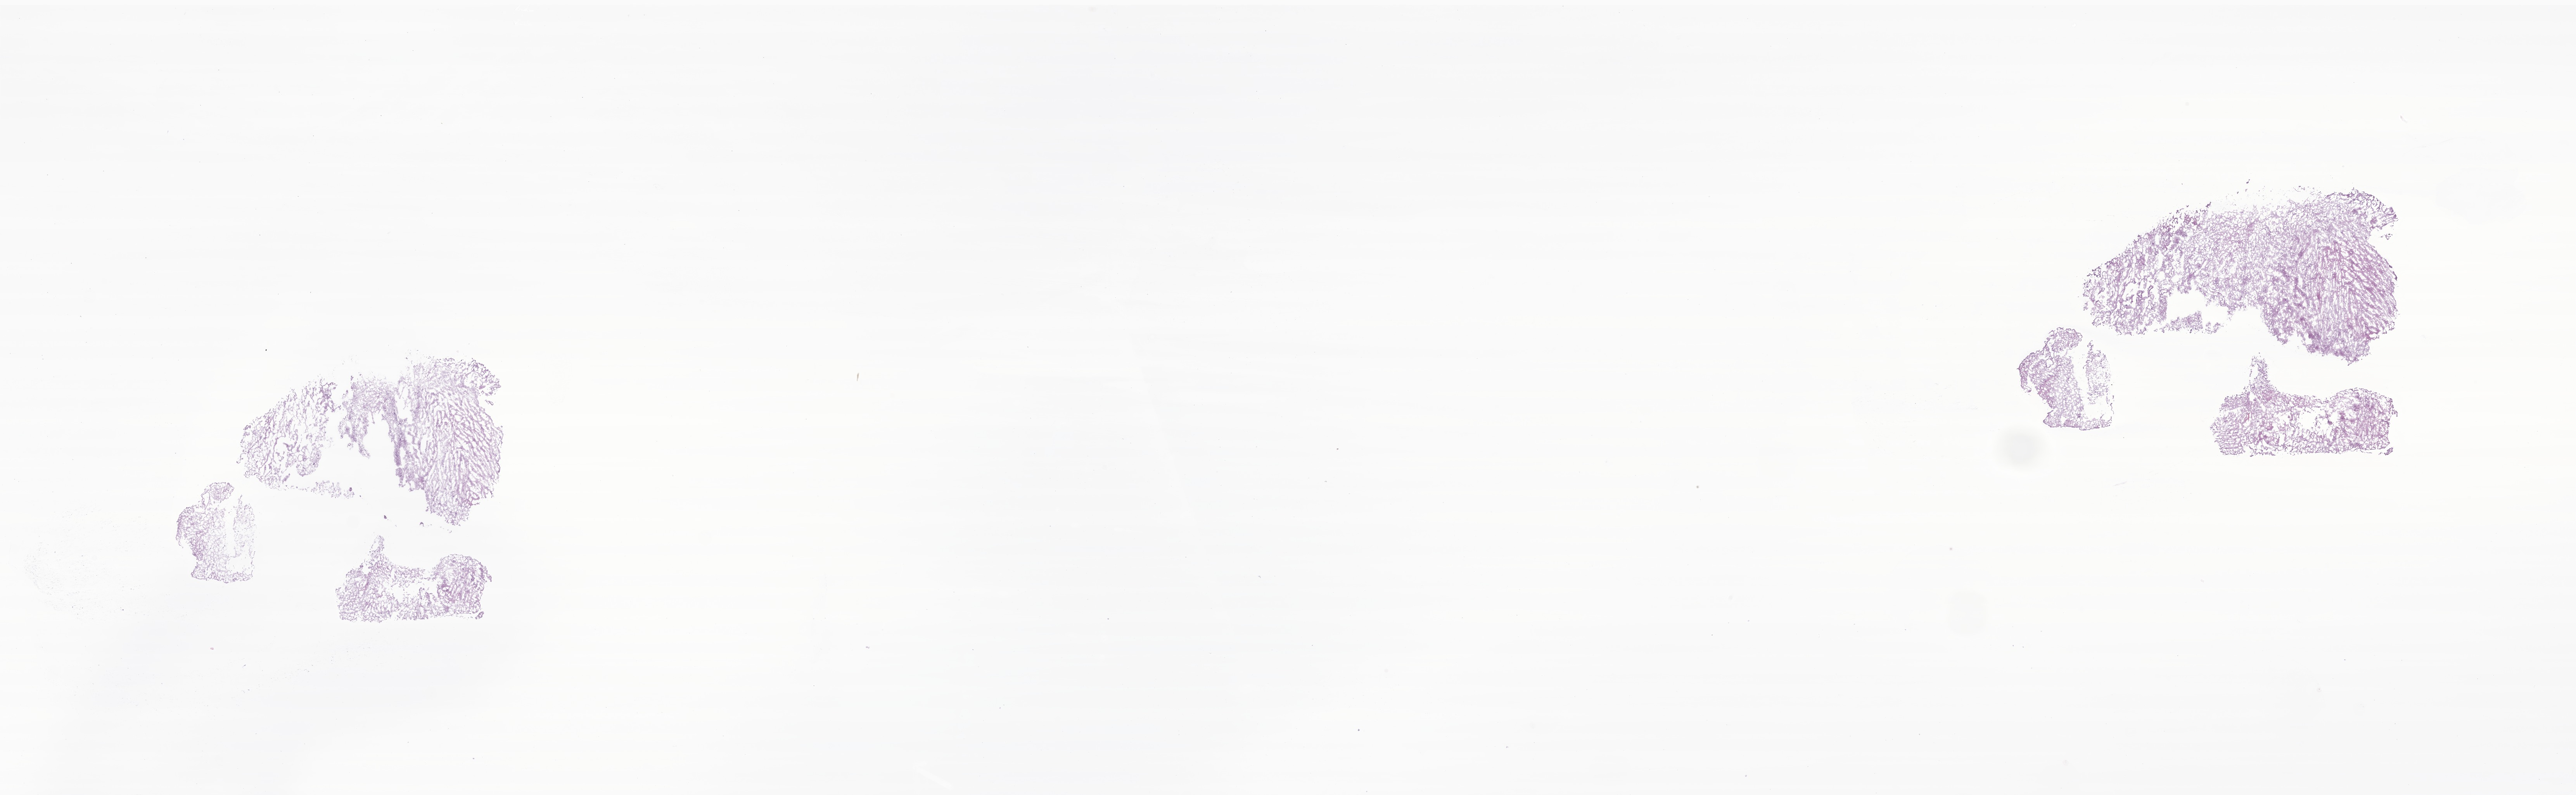
Whole-slide image, haematoxylin and eosin stain of tumor tissue from the spinal cord — shown as a low-resolution overview of the whole scanned area (about 28.0 x 8.6 mm). Cryosection (OCT / tissue freezing medium). Male patient, age 195 months (16 years 3 months).
Recorded diagnosis: Pilocytic astrocytoma.